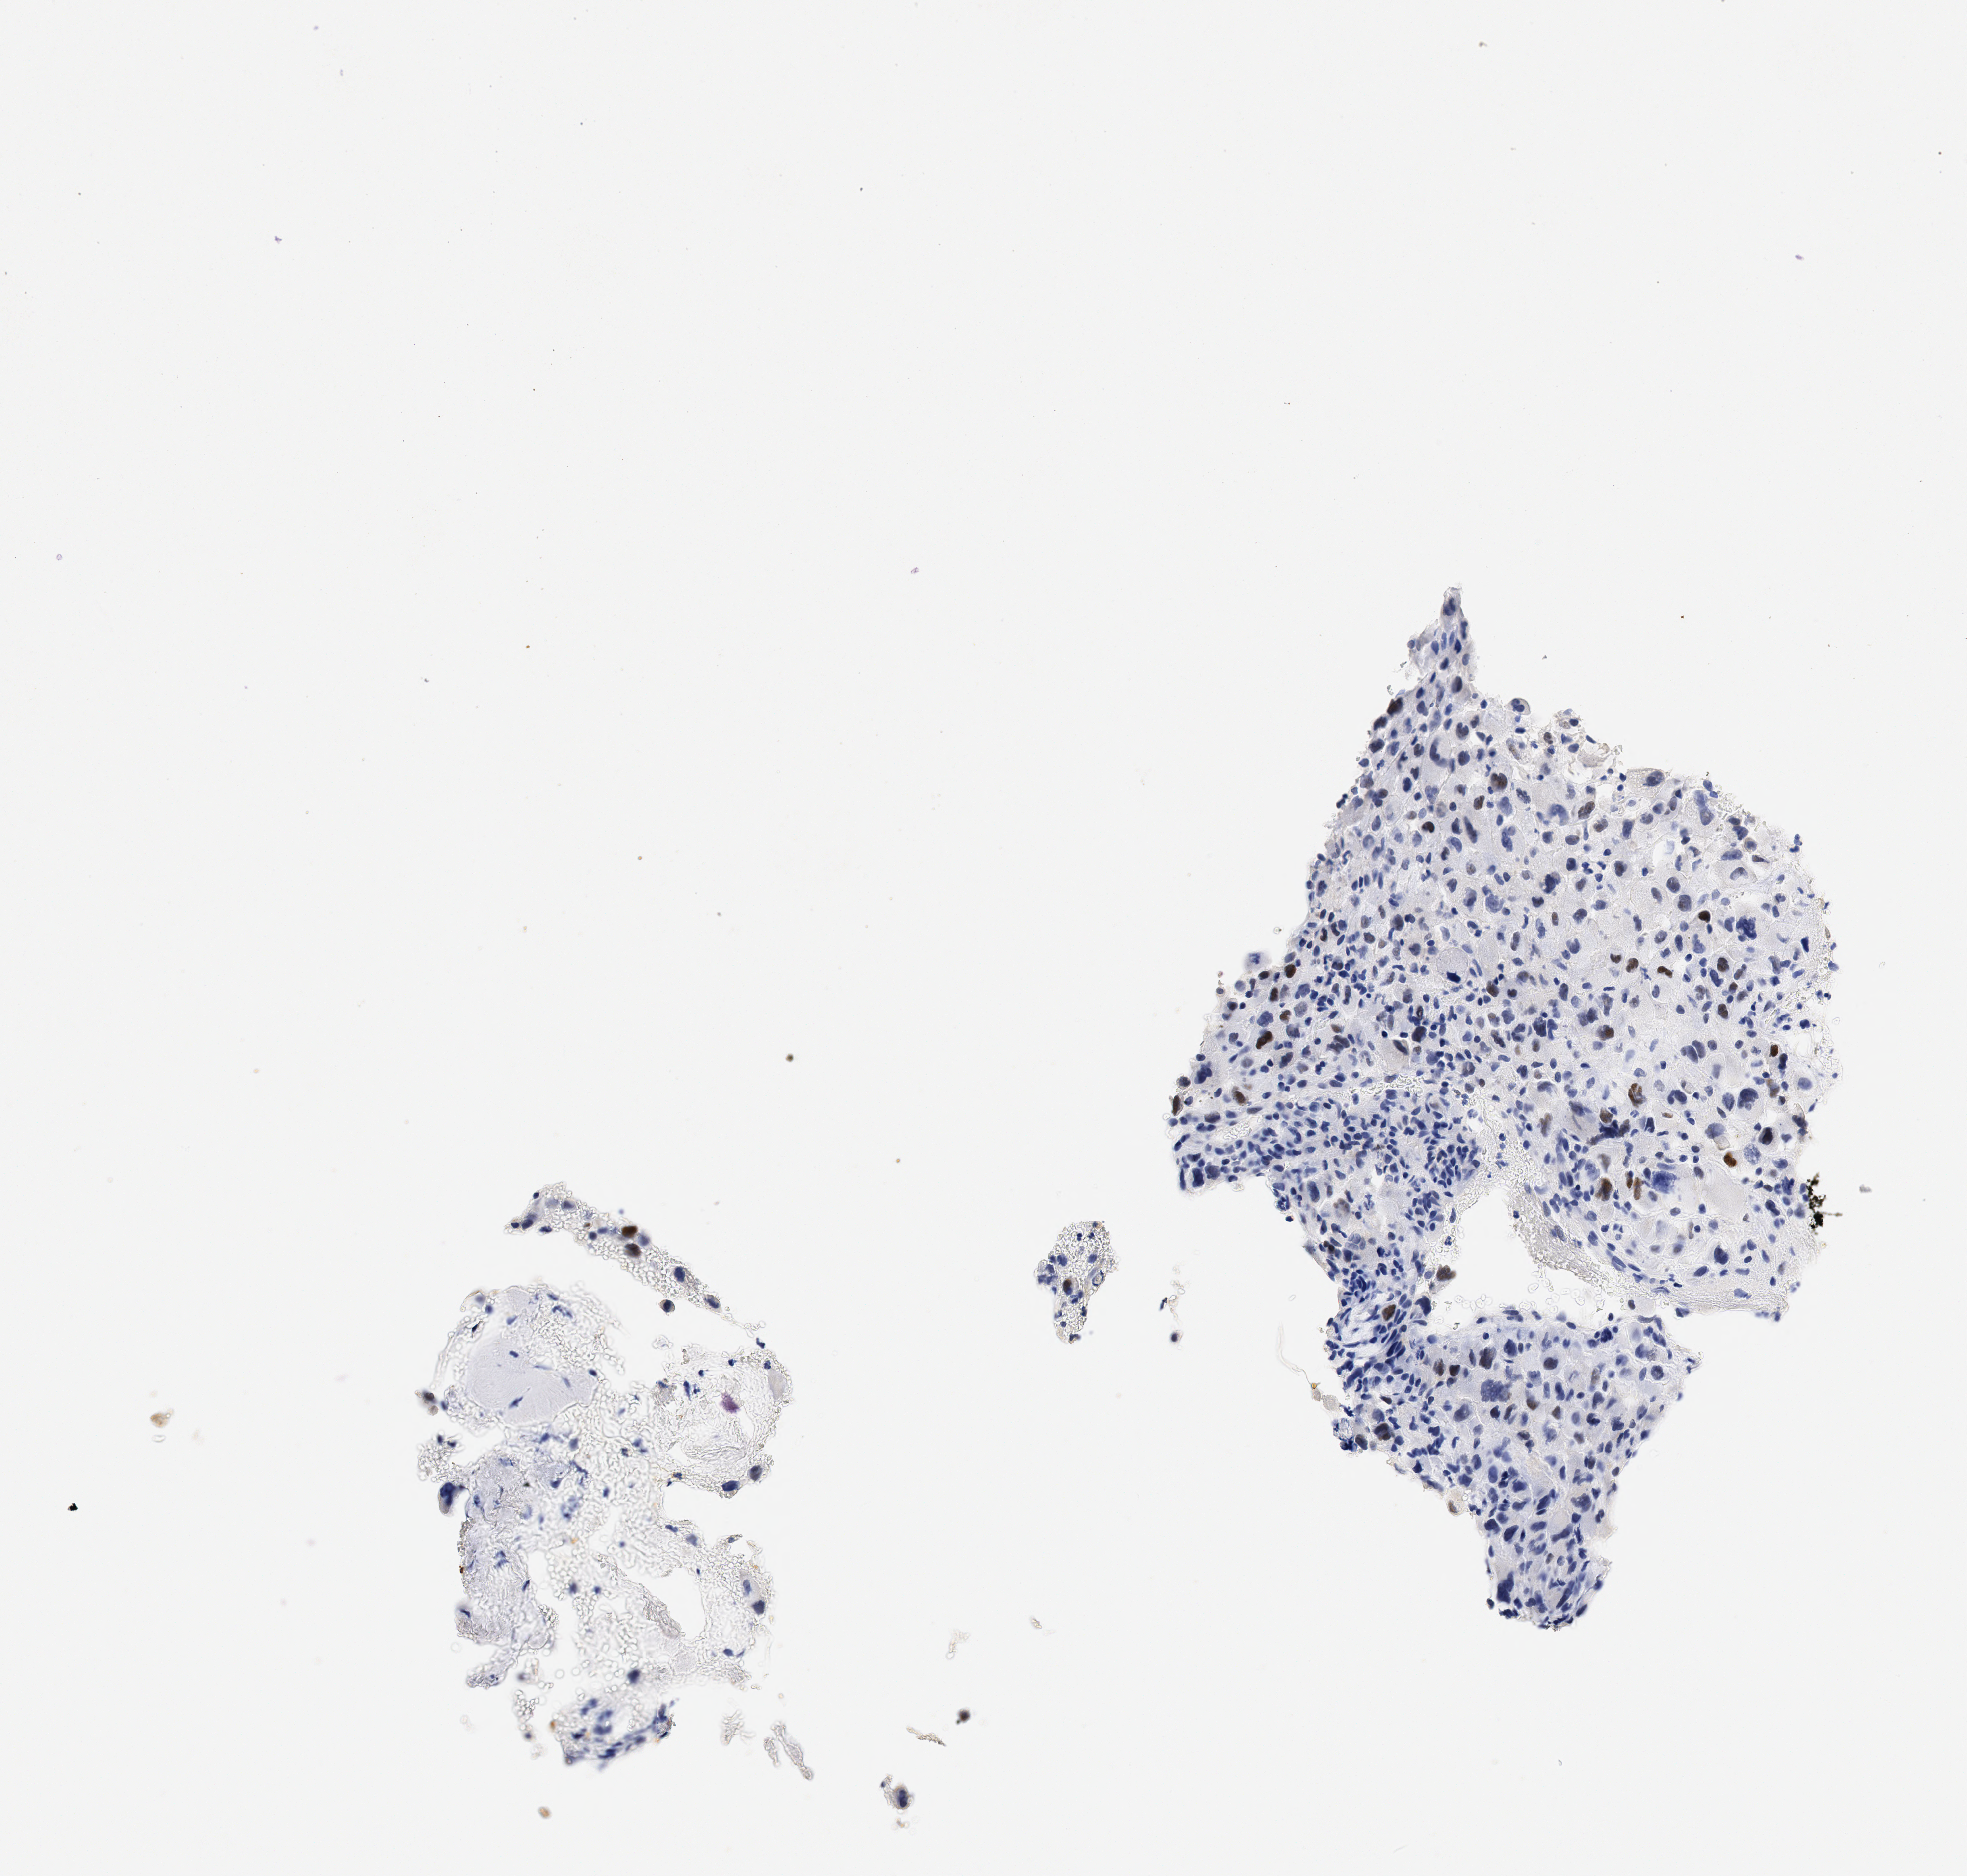
IHC for TTF-1 (thyroid transcription factor 1), whole-slide image, shown at full scan resolution across the whole scanned area, about 1.5 x 1.4 mm. Tumor tissue. Anatomic site: lung (right). Patient: male, aged 63.
Diagnosis: Adenocarcinoma, NOS.